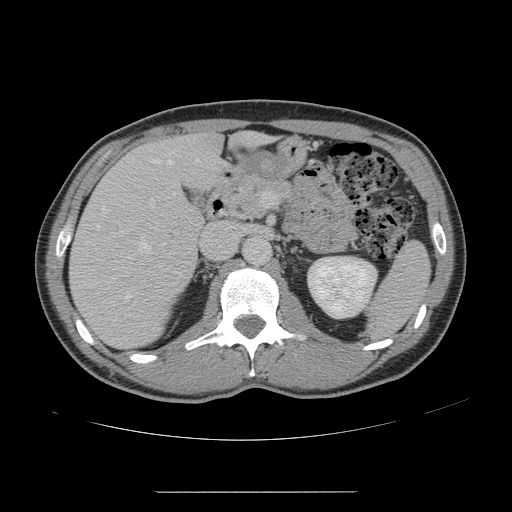
Contrast-enhanced abdominal CT, one axial slice; position 82 of 178 along the scan axis; intravenous contrast given; soft-tissue window (W 400 / L 40 HU); 512 × 512 image matrix, field of view 401 × 401 mm. Male patient, age 53 years. From the clinical record (not read from this slice): diagnosis: colorectal cancer liver metastases, imaged before liver resection; multiple liver metastases: yes; largest metastasis: 2.4 cm; disease in both lobes: no.
Annotated regions visible in this slice (manually delineated by an expert):
- hepatic veins: bounding box <97,159,199,302> (left, top, right, bottom; pixels)
- liver: <71,133,267,348>
- planned liver remnant (the part of the liver to remain after resection): <157,133,266,188>
- portal vein (with intrahepatic branches): <149,192,267,268>